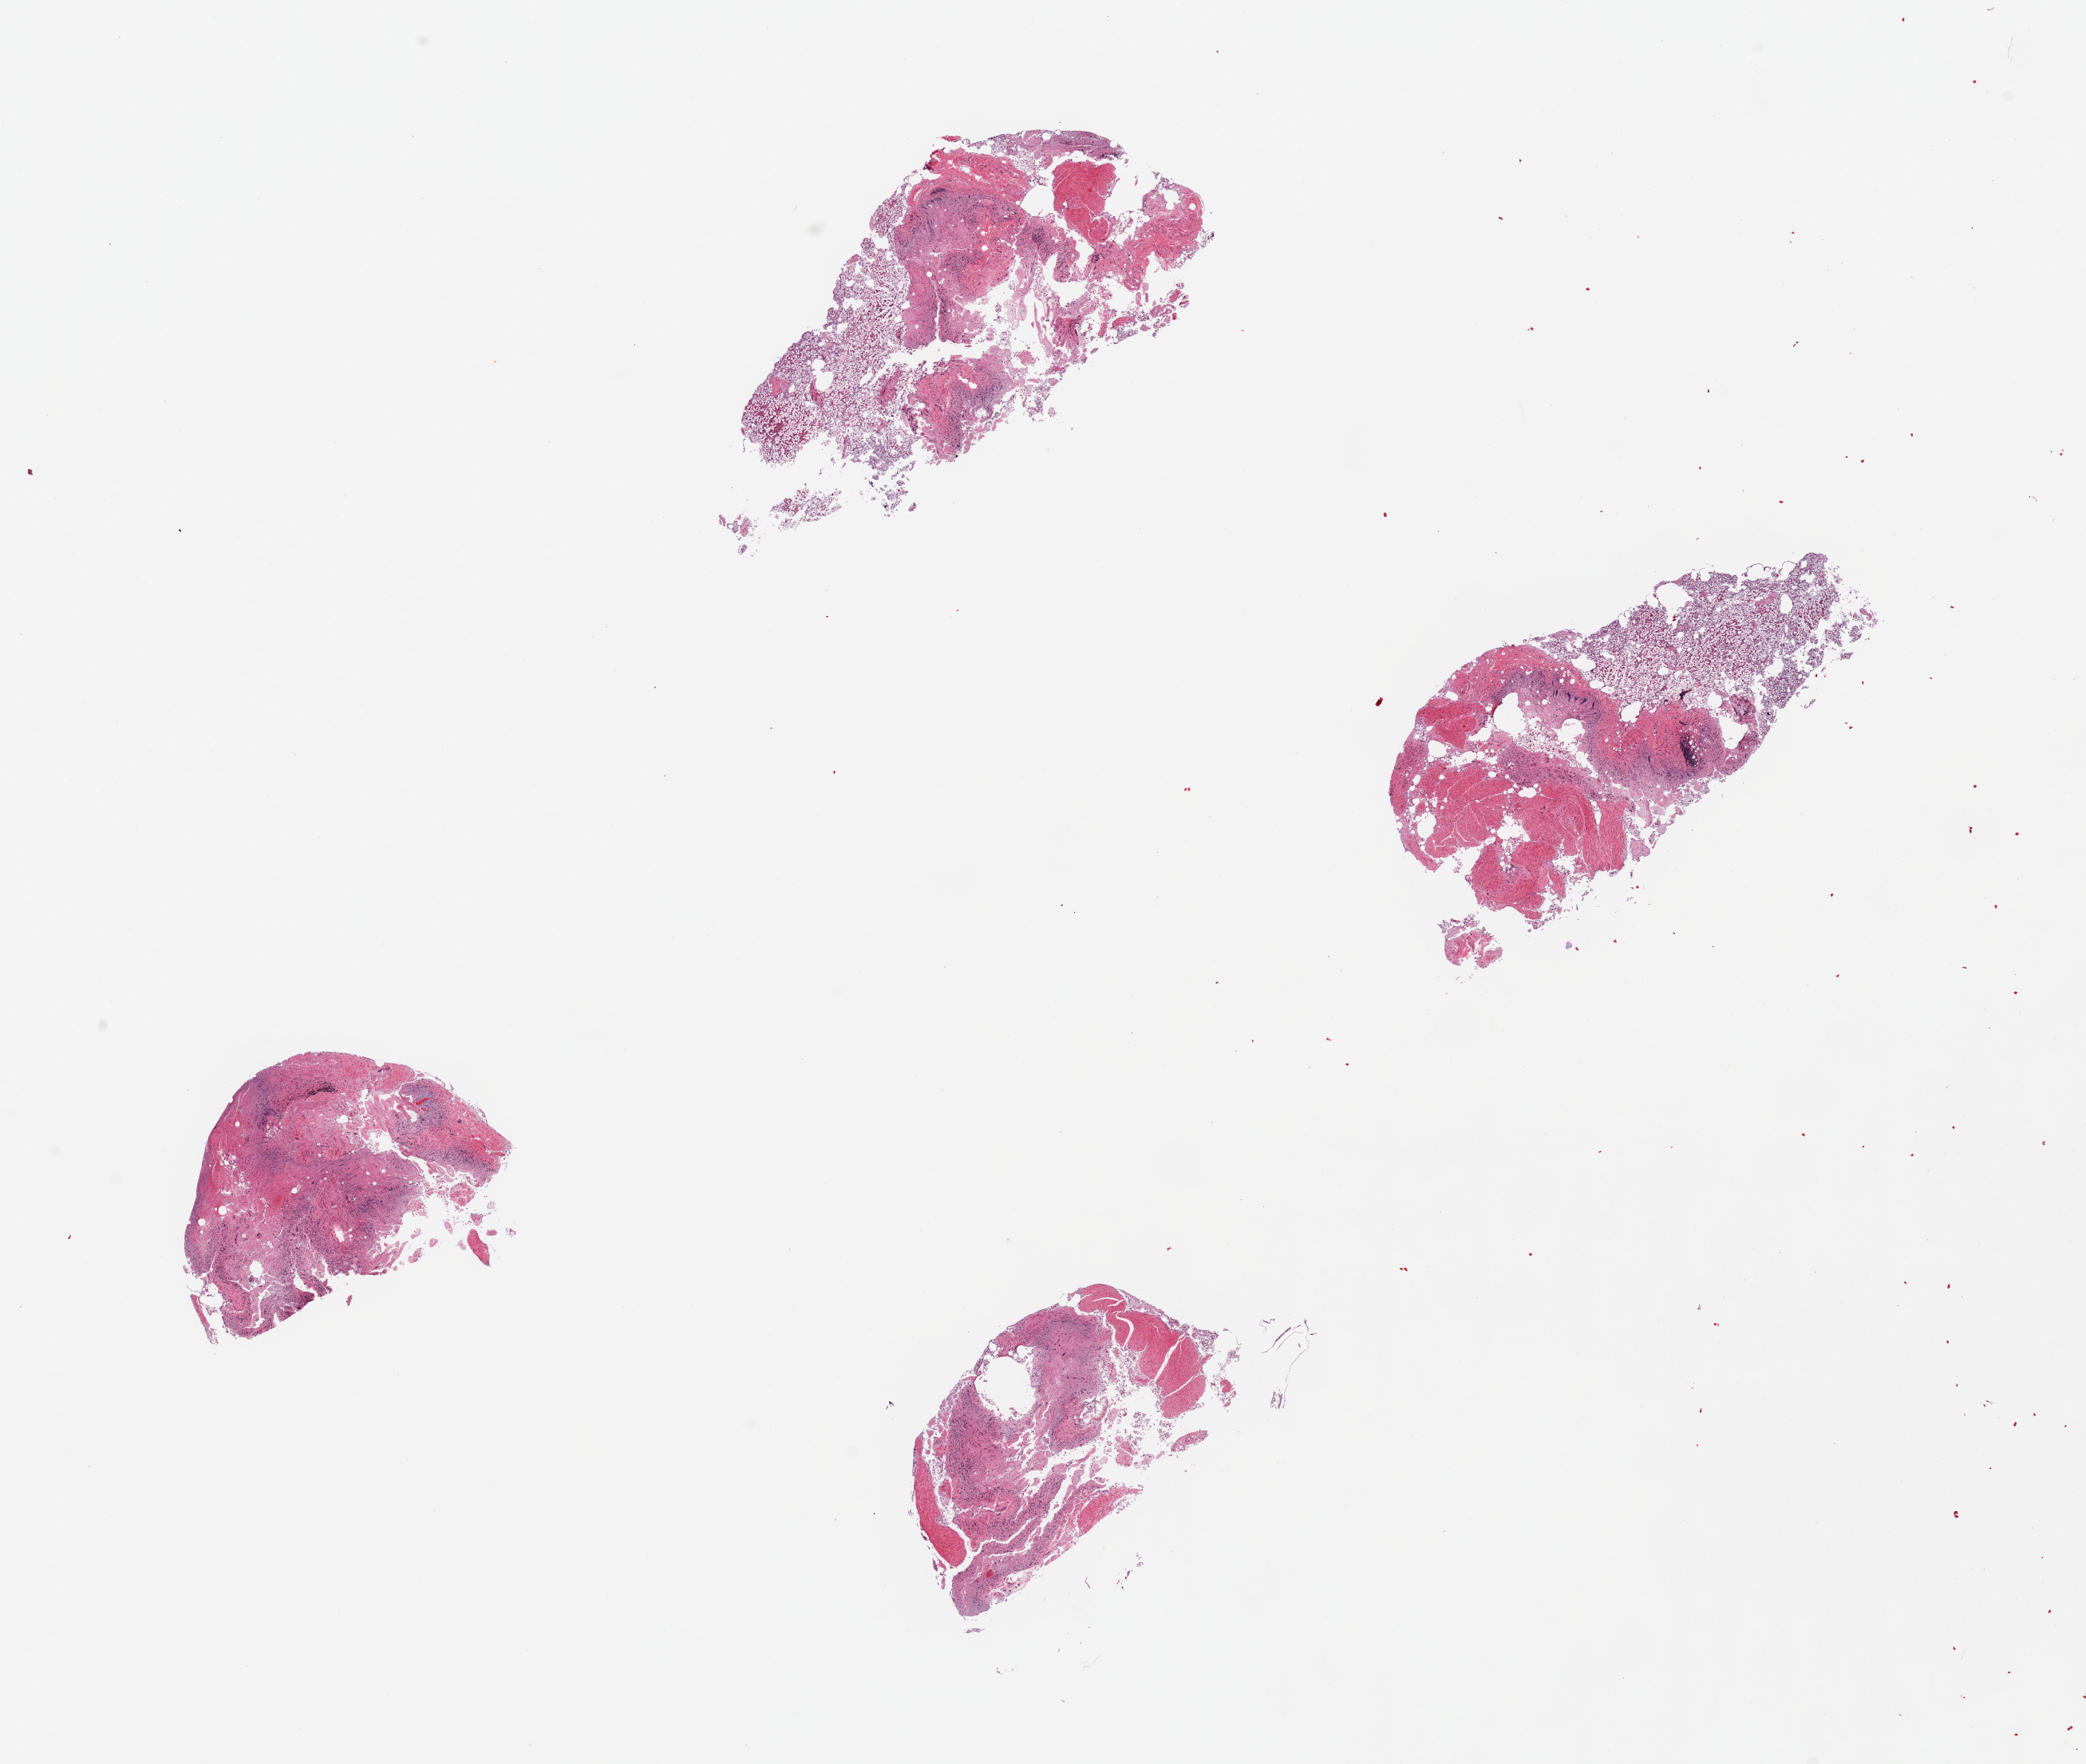
Digitized hematoxylin and eosin (H&E)-stained section — shown as a low-resolution overview of the whole scanned area (about 20.7 x 17.5 mm). PAXgene-fixed, paraffin-embedded tissue. Section of ileum (target tissue). Donor tissue sample. Male donor.
* reviewer comment on this tissue sample: 4 pieces; fragments of autolyzed mucosa and muscularis (not target) with no significant residual lymphoid tissue (target)